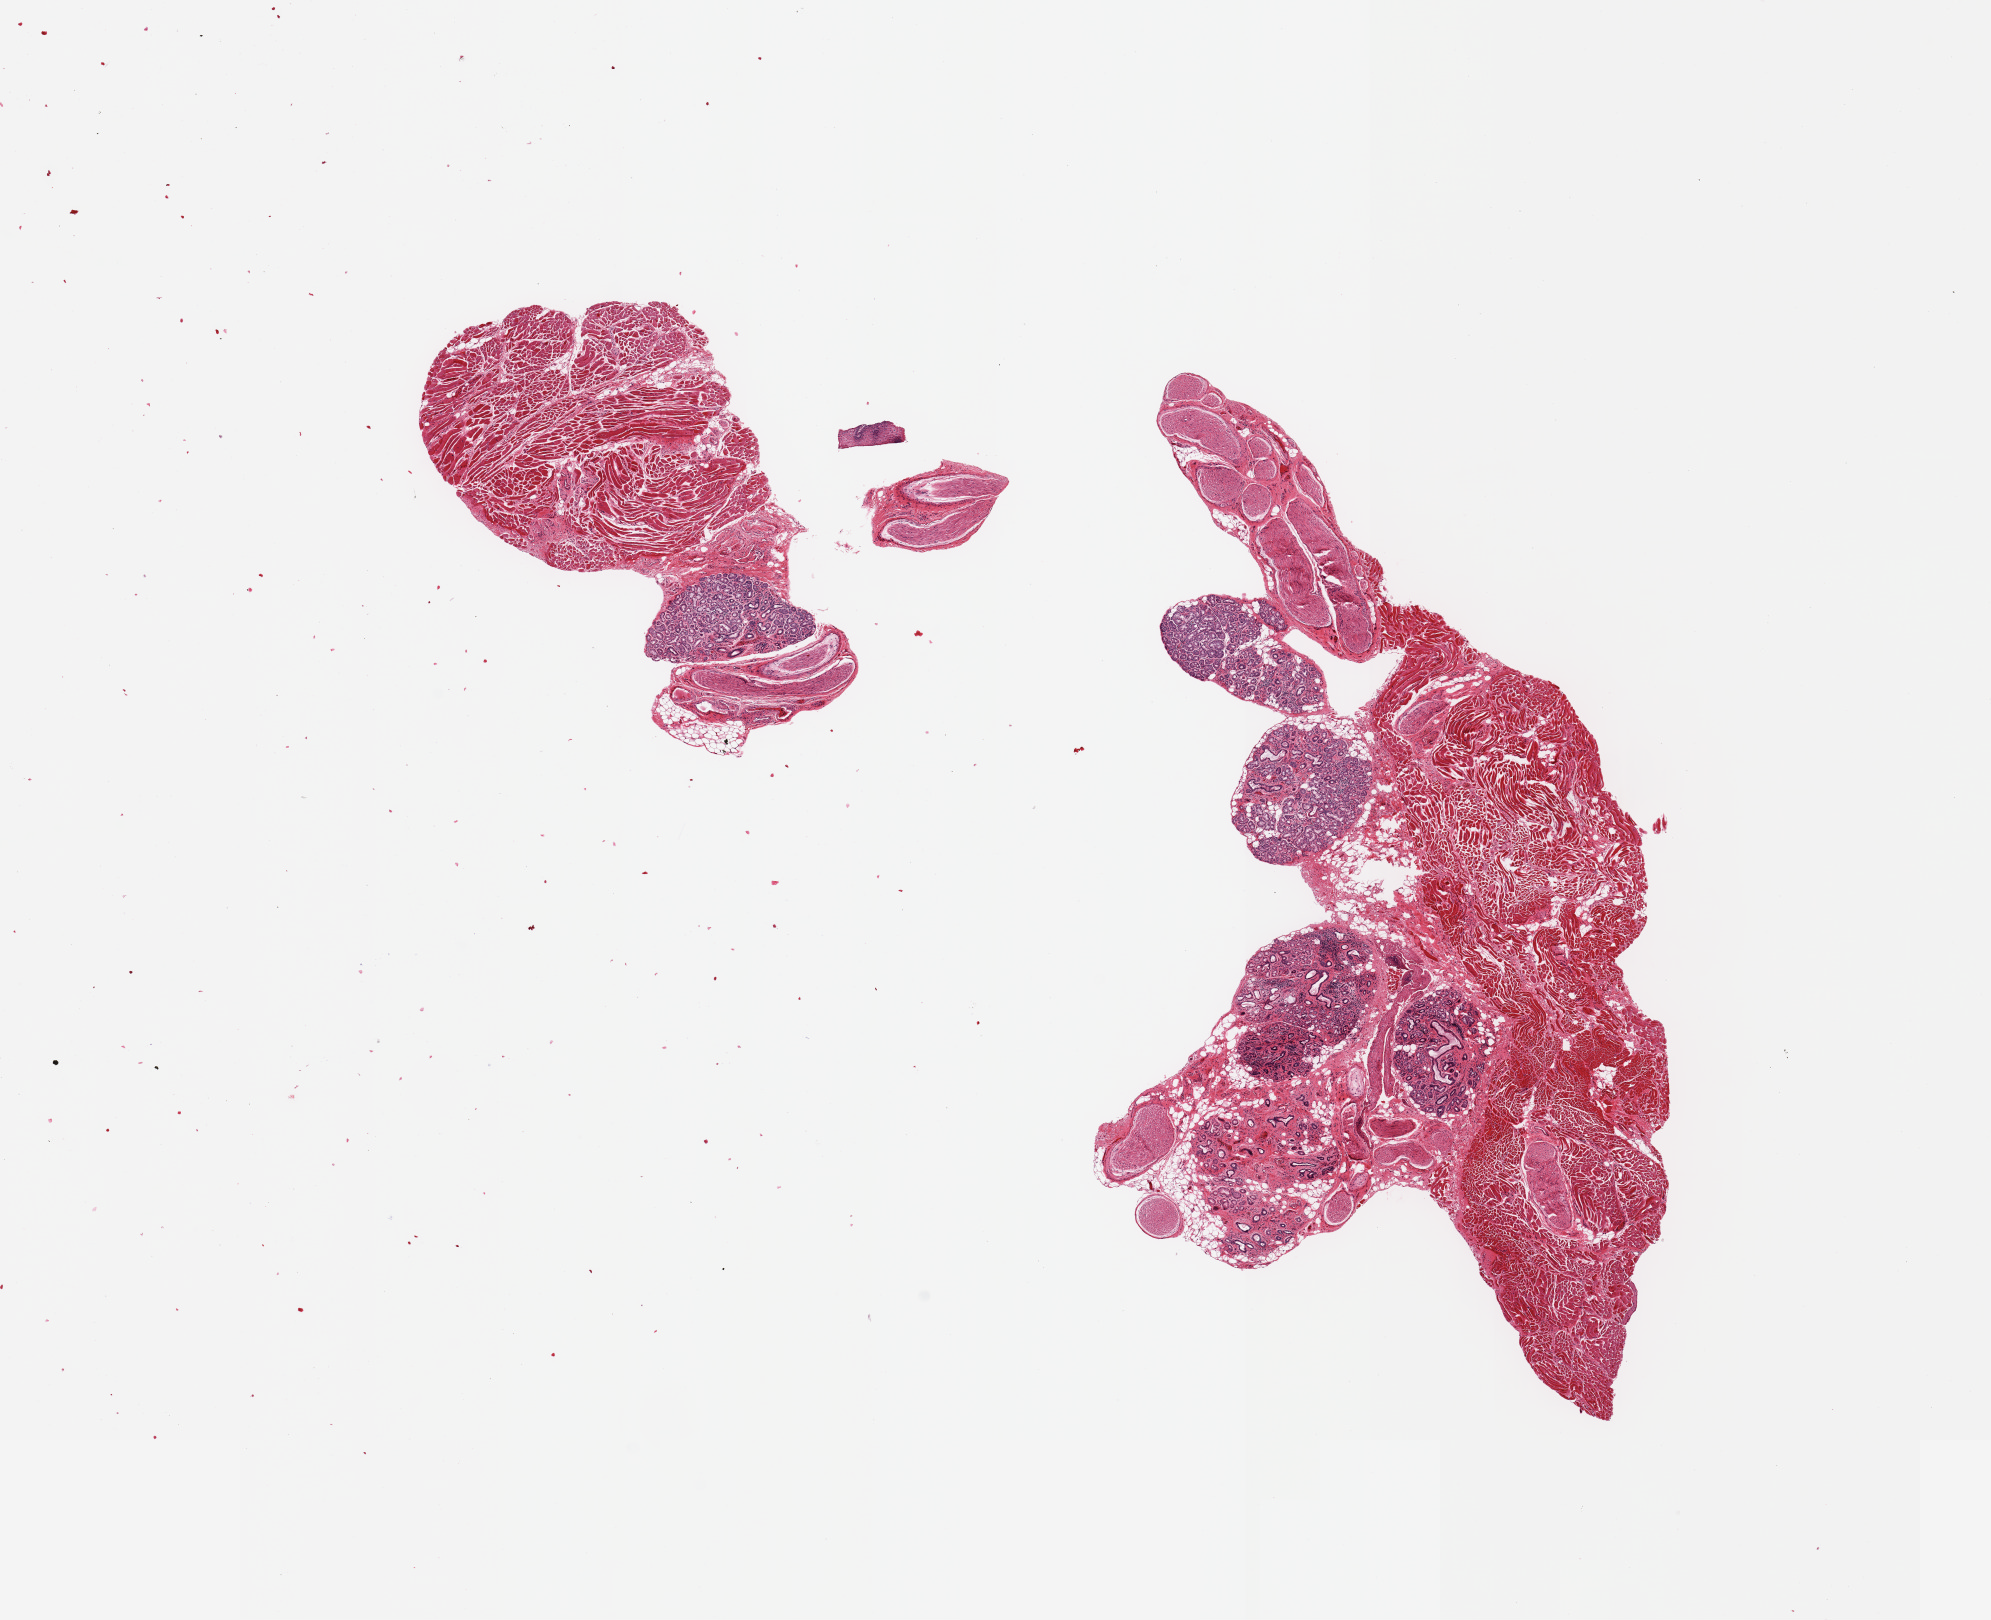
Digitized haematoxylin and eosin-stained section — a low-resolution overview of the entire scanned area, about 15.8 x 12.8 mm (from a 20x scan). PAXgene-fixed paraffin-embedded (PFPE) section. Section of minor salivary gland (target tissue). Donor tissue sample. Donor: male.
Reviewer comment on this tissue sample: 2 pieces, glandular elements are ~40% of tissue rest is stroma/skeletal muscle.